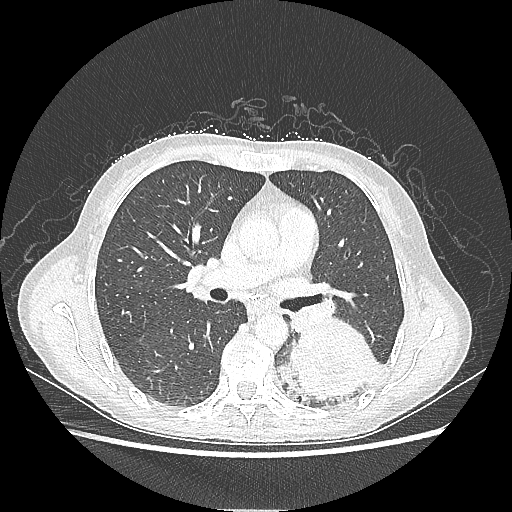
Chest CT, one axial slice; slice 125 of 220 in the series (ordered by position); reconstruction kernel LUNG; 80 kVp; lung window (W 1500 / L -600 HU); 1.25 mm slice thickness; 512 × 512 image matrix. Female patient, age 53 years. From the clinical record (not read from this slice): clinical TNM (as recorded): T3 N0 M0.
Structures marked on this image (bounding box drawn by a radiologist):
- lung tumour (recorded histology: adenocarcinoma): box from (x=281, y=319) to (x=380, y=404) px